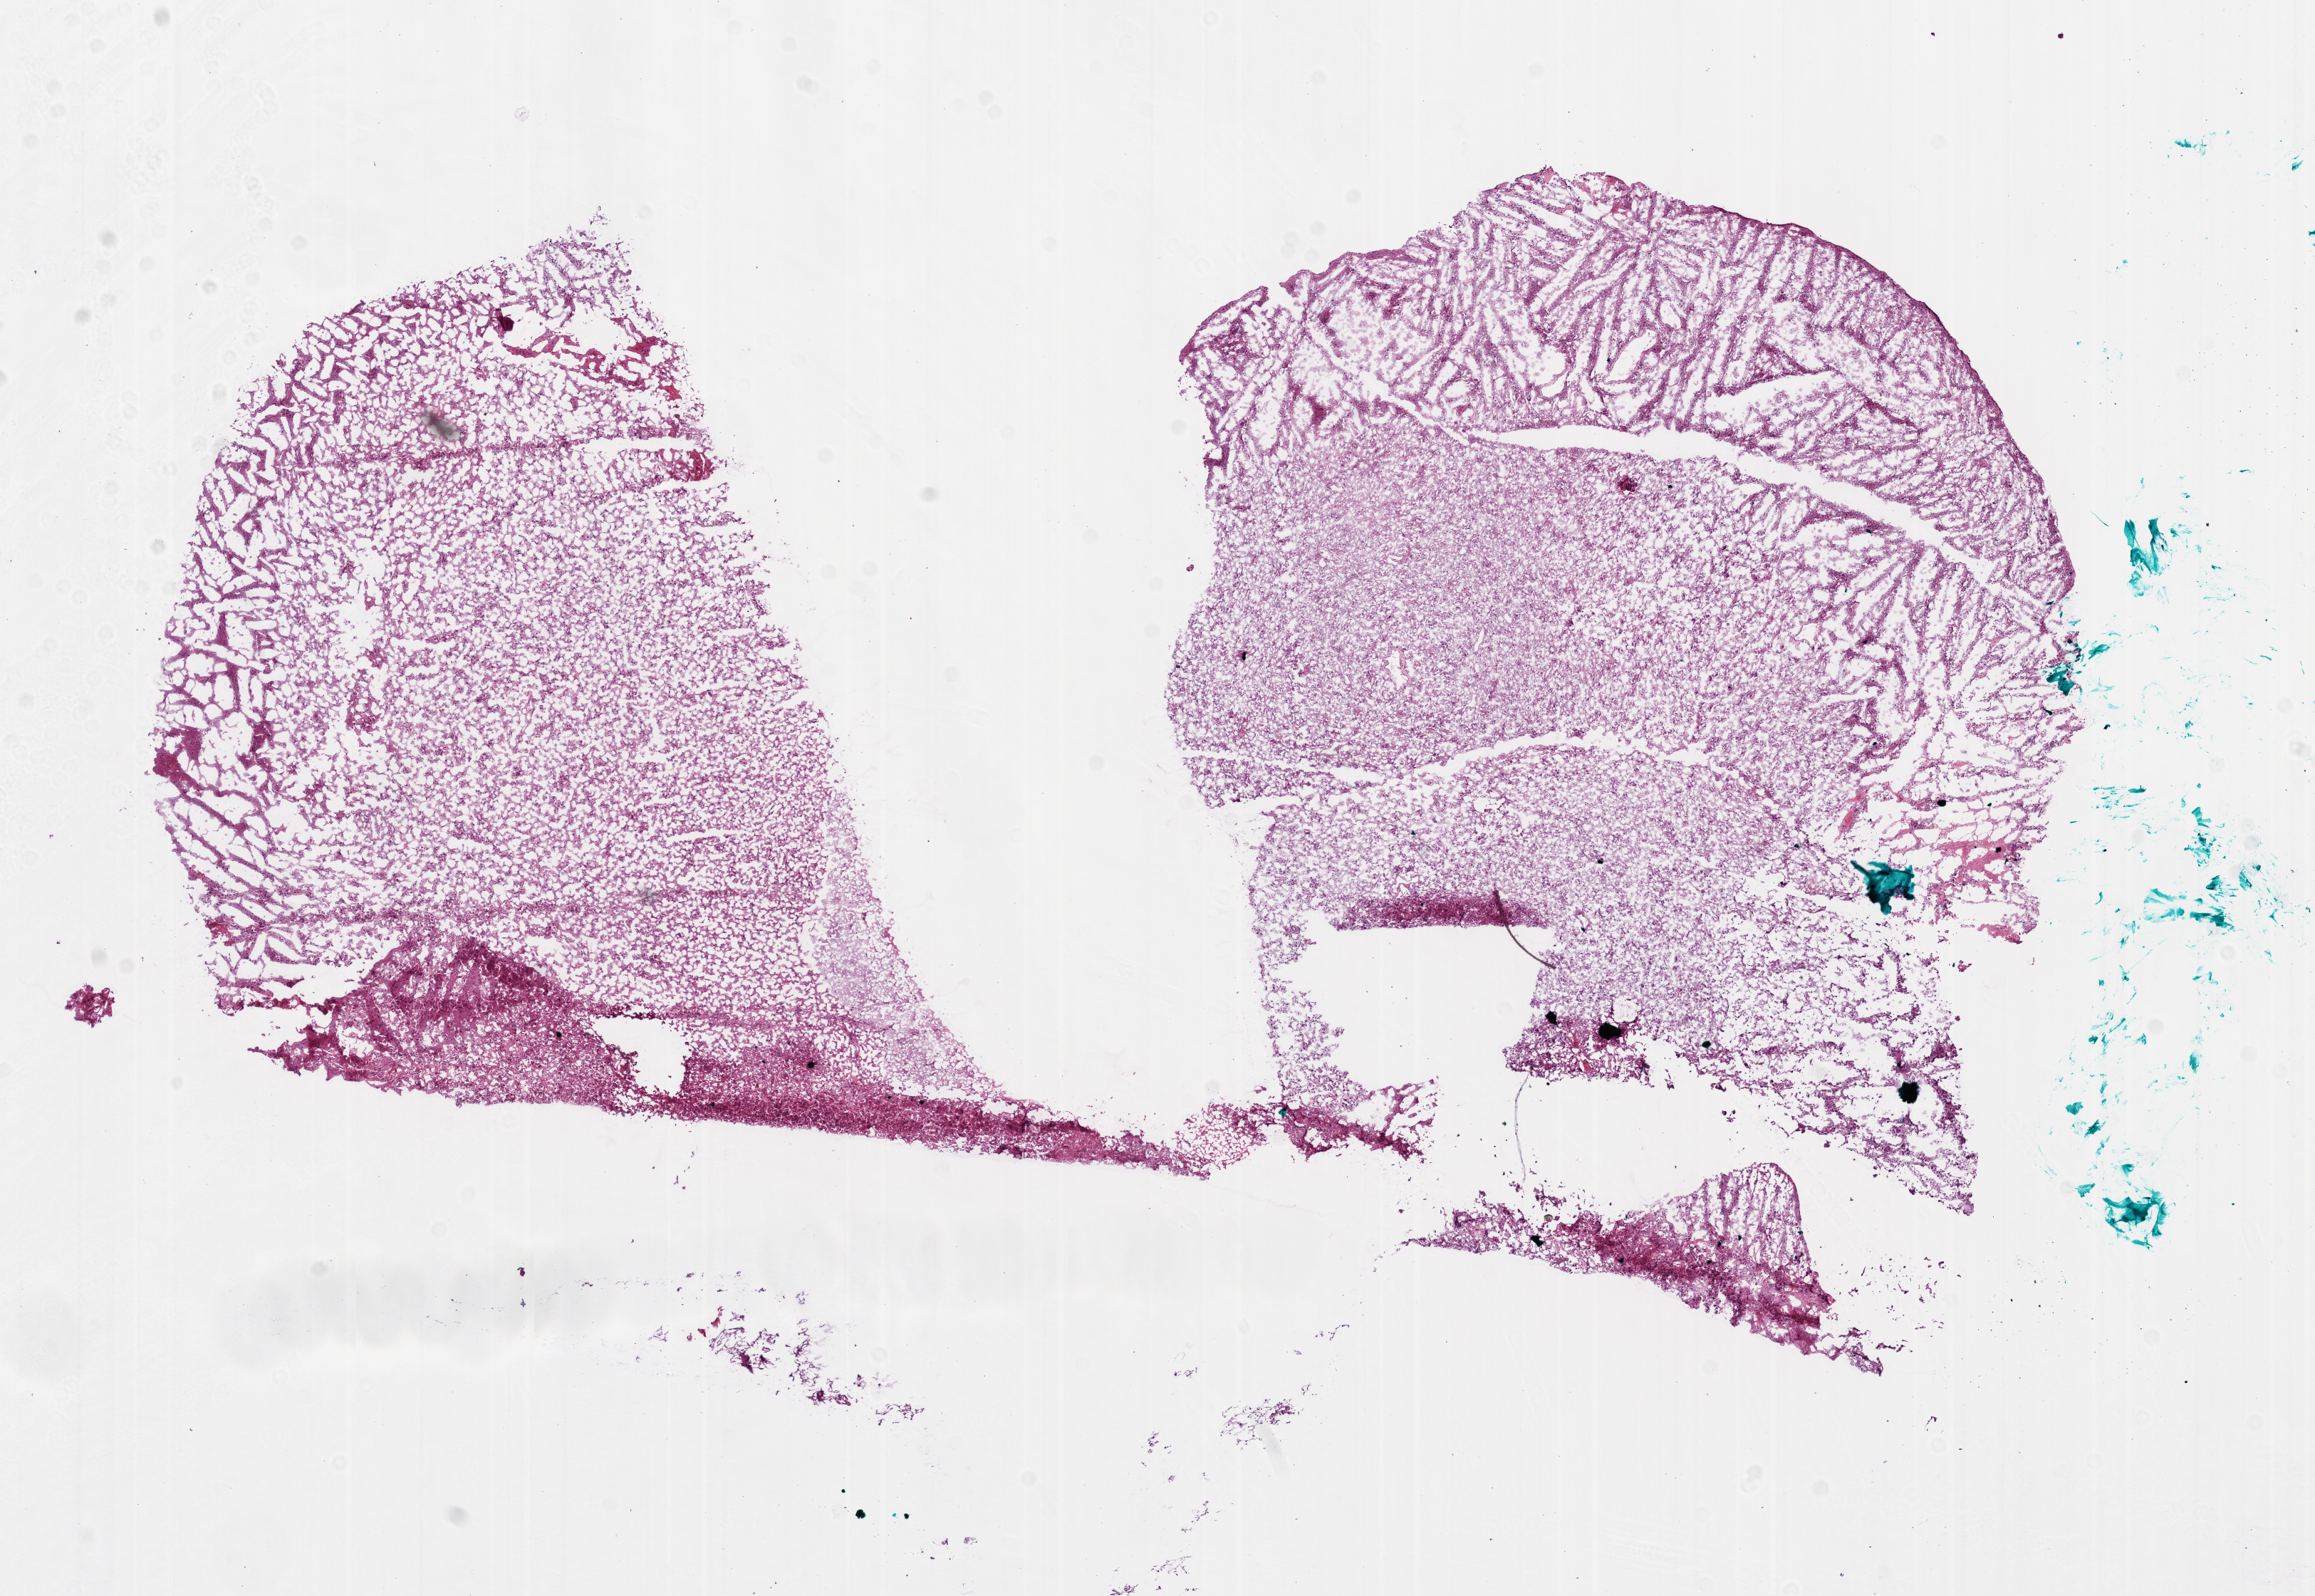
Whole-slide histology image, H&E-stained, low-resolution overview of the scanned area, about 13.0 x 9.0 mm (acquisition: 20x scan), frozen section from the bottom of the tissue portion, brain, primary tumour sample. Patient: male, age at initial diagnosis 46 years. Pathologist review of this section (percent, as recorded): tumour cells 100%, tumour nuclei 100%, normal cells 0%, stromal cells 0%, necrosis 0%. Infiltration values recorded for this section: lymphocyte infiltration 0%.
Diagnosis: Glioblastoma.